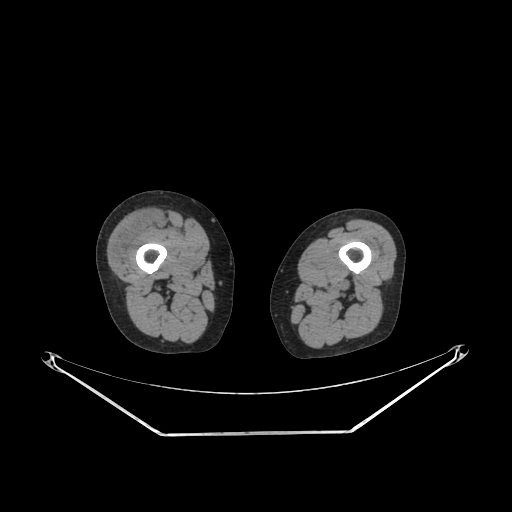
CT of an extremity soft-tissue mass (from a PET/CT study), one axial slice. Position 212 of 311 along the scan axis. Reconstruction kernel SOFT. Soft-tissue window (W 400 / L 40 HU). 3.75 mm slice thickness. 512 × 512 image matrix, field of view 500 × 500 mm. Female patient. Case-level facts recorded for this patient, not image findings: histological type: pleiomorphic undifferentiated sarcoma; grade: high; site of the primary tumour: right quadricep.
Outlined on this slice (expert contour drawn on MRI and transferred to this co-registered scan by the dataset authors):
- tumour plus oedema (research contour): bounding box [x1, y1, x2, y2] px = [112, 210, 161, 261]